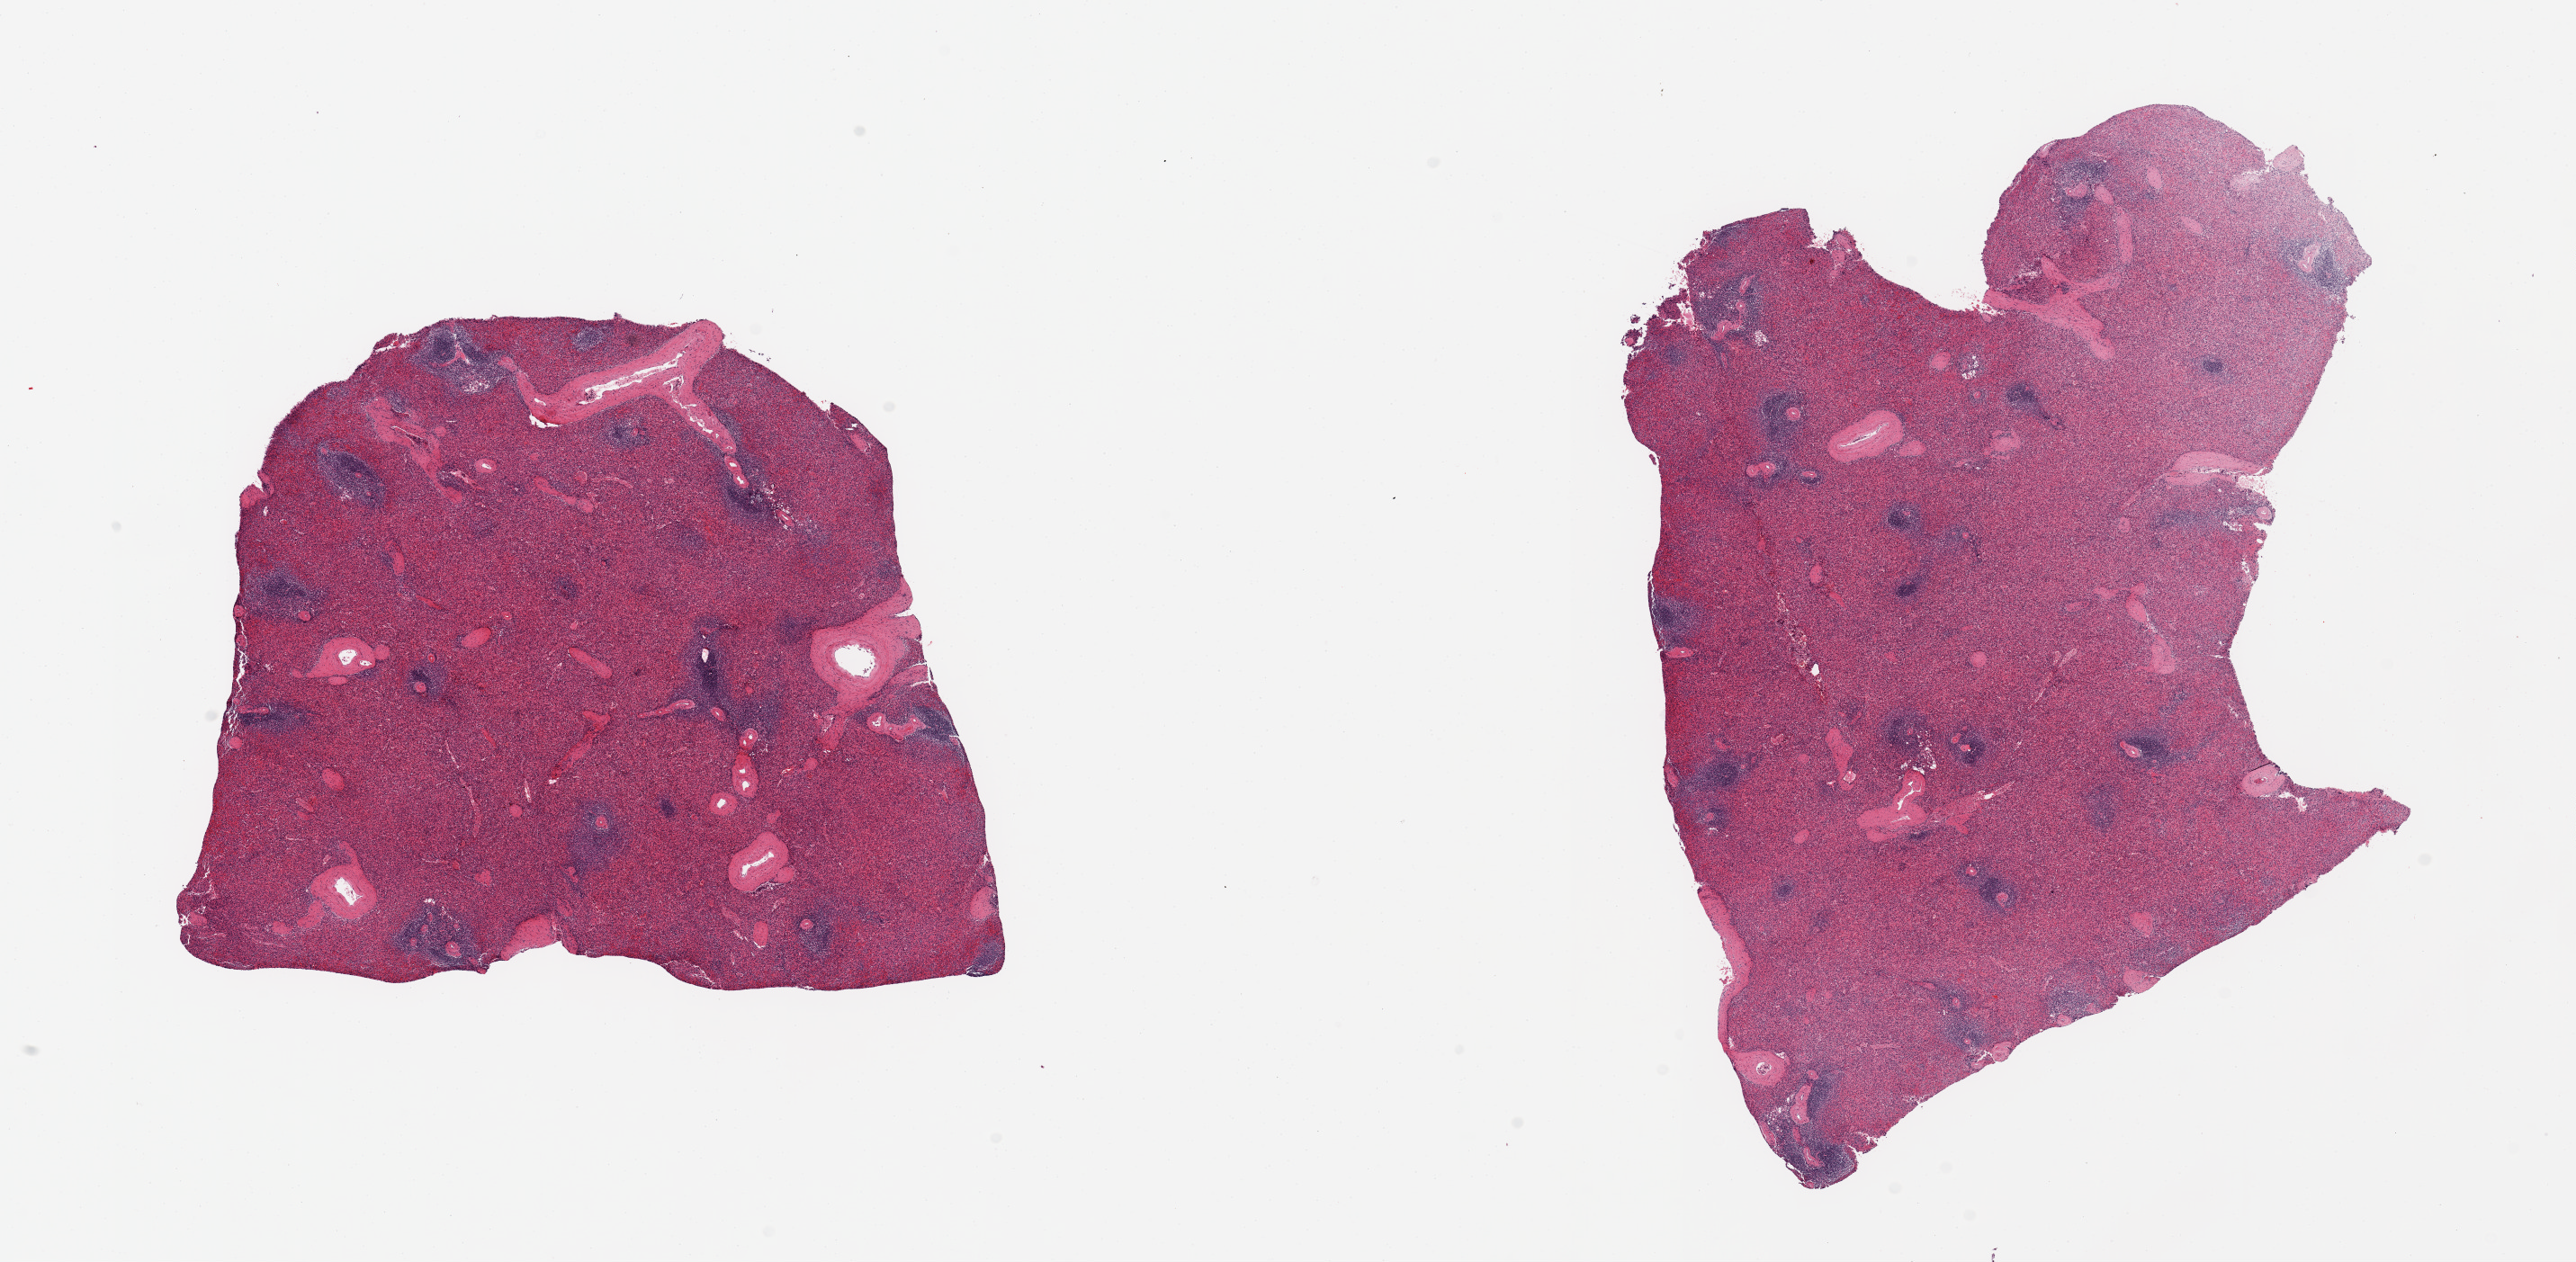
H&E whole-slide image — whole scanned area (about 22.6 x 11.1 mm) shown as a low-resolution overview, PAXgene-fixed, paraffin-embedded tissue, target tissue: spleen, tissue donor sample. Male donor.
Reviewer comment on this tissue sample: 2 pieces; mild congestion.